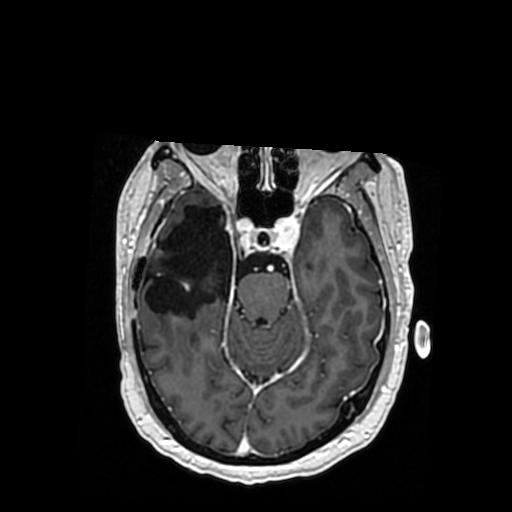
Brain MRI from a brain-tumour surgery series, one axial slice. Slice 226 of 364 in the series (ordered by position). T1-weighted post-contrast. 0.5 mm slice thickness. 512 × 512 image matrix, field of view 260 × 260 mm. Case-level facts recorded for this patient, not image findings: histopathology: Oligodendroglioma; WHO grade: 3; IDH mutation: yes.
Outlined on this slice (expert manual segmentation):
- previous resection cavity: bounding box <144,206,233,317> (left, top, right, bottom; pixels)